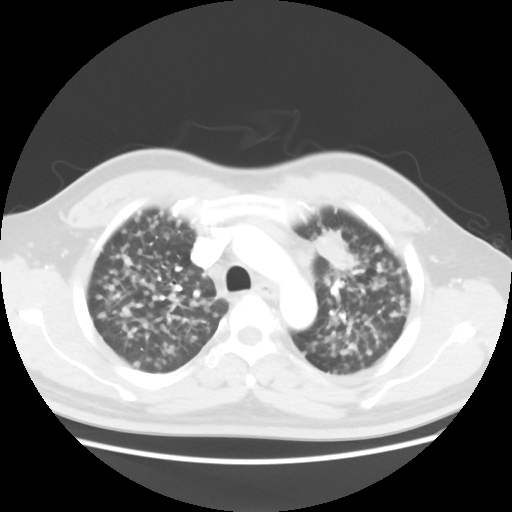
Chest CT, one axial slice. Slice 29 of 40 in the series (ordered by position). 120 kVp. Lung window (W 1500 / L -600 HU). 5 mm slice thickness. 512 × 512 image matrix, field of view 366 × 366 mm. Male patient, age 41 years. From the clinical record (not read from this slice): clinical TNM (as recorded): T1c N3 M1b.
Annotated regions visible in this slice (bounding box drawn by a radiologist):
- lung tumour (recorded histology: adenocarcinoma): box from (x=312, y=230) to (x=354, y=275) px